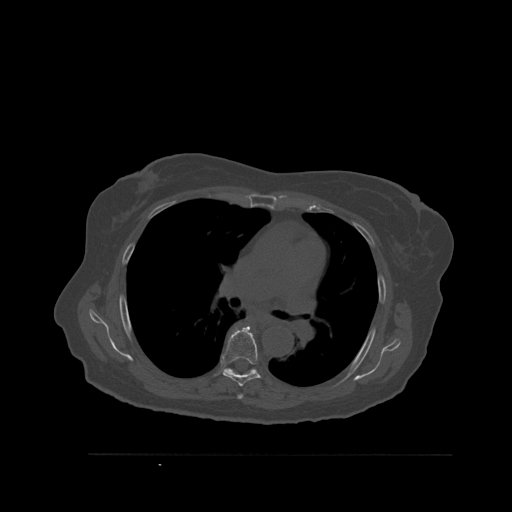
CT including the spine, one axial slice; slice 379 of 527 in the series (ordered by position); bone window (W 1800 / L 400 HU); 1.5 mm slice thickness; 512 × 512 image matrix. Female patient, age 73 years. Case-level facts recorded for this patient, not image findings: primary cancer: breast; vertebrae with lytic lesions (as recorded): L2.
Structures marked on this image (semi-automatic segmentation, software-assisted and operator-edited):
- T5 vertebra: bounding box (x1, y1, x2, y2) in pixels: (237, 394, 243, 399)
- T6 vertebra: (221, 326, 261, 387)
- T7 vertebra: (232, 370, 253, 375)